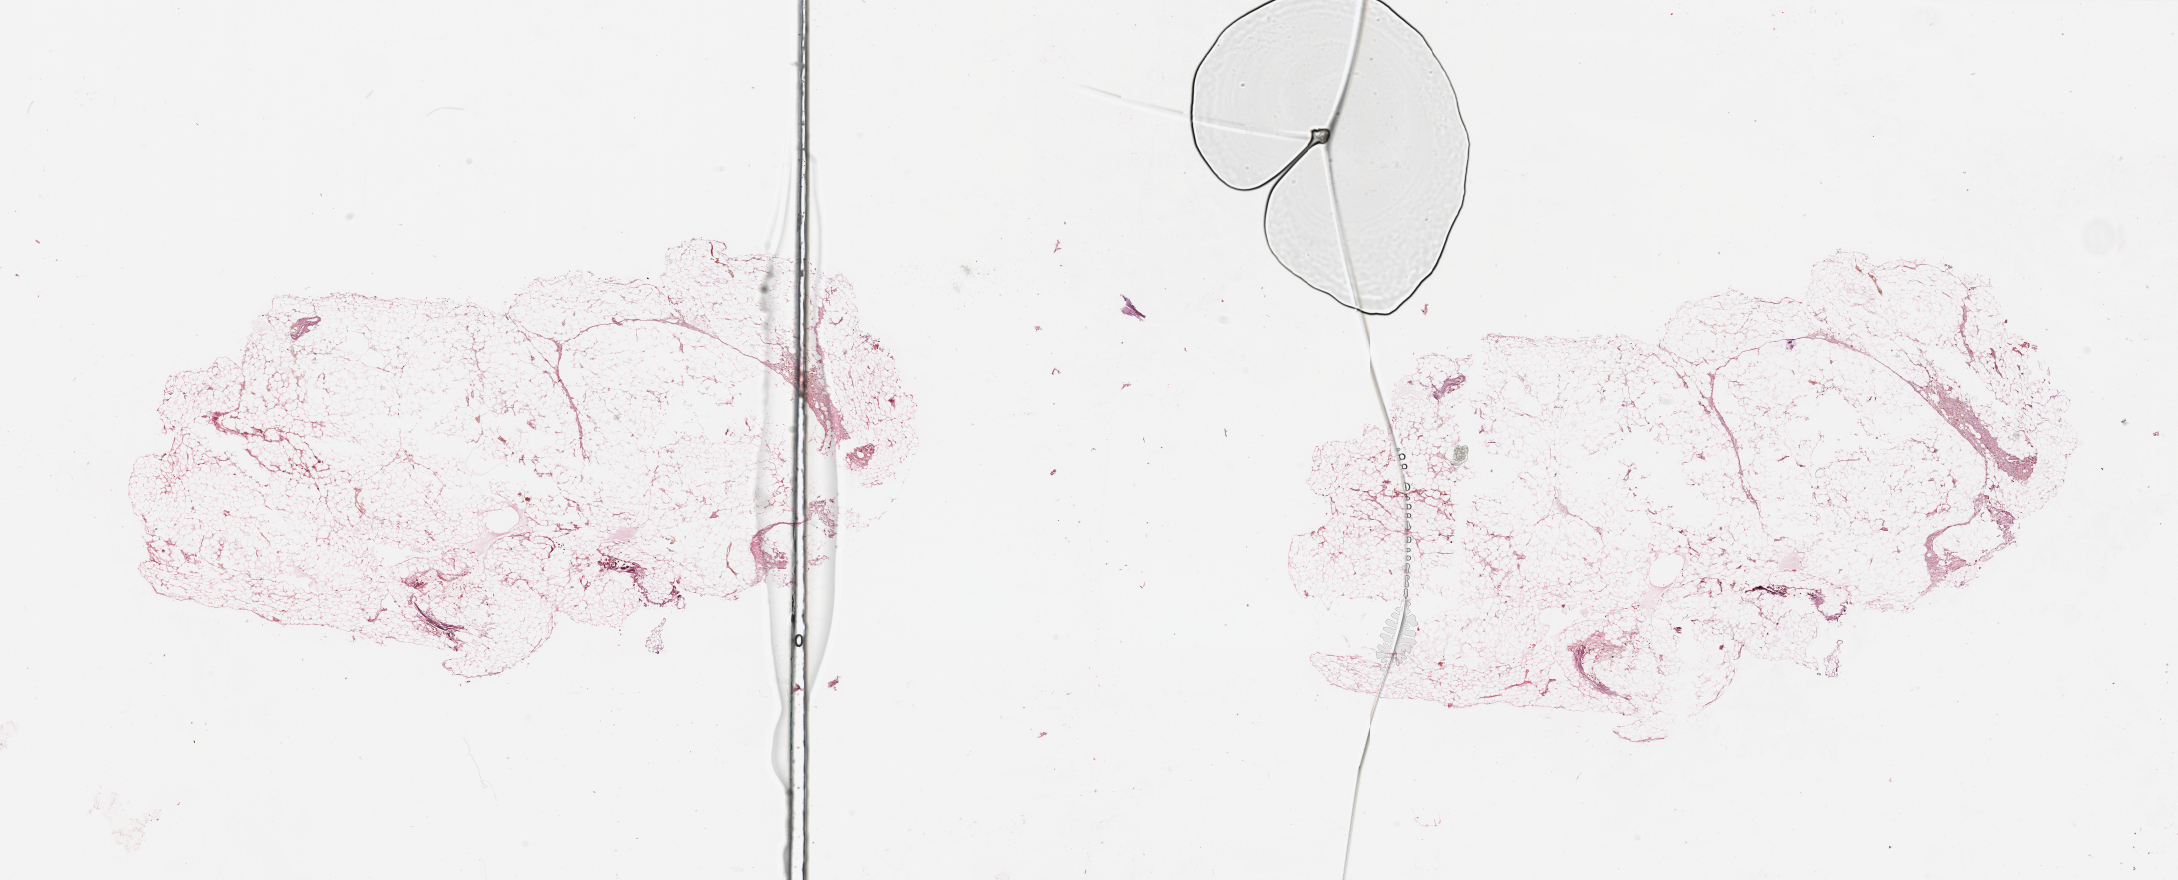
H&E-stained whole-slide image, shown as a low-resolution overview of the whole scanned area (about 34.5 x 13.9 mm, from a 20x scan), normal (non-tumour) tissue sample, sampled site: skin. Patient: female, age 67 years.
This section: normal (non-tumour) tissue from the same patient. Patient diagnosis: Malignant melanoma, NOS.